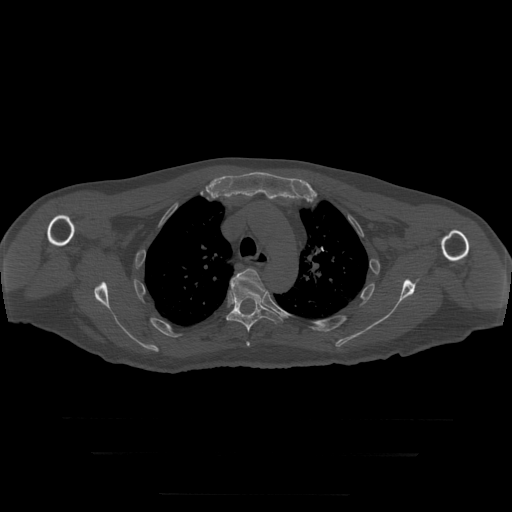
CT including the spine, one axial slice. Slice 229 of 397 in the series (ordered by position). Reconstruction kernel STANDARD. Bone window (W 1800 / L 400 HU). 512 × 512 image matrix, field of view 510 × 510 mm. Patient age 73 years. Case-level facts recorded for this patient, not image findings: primary cancer: prostate.
Structures marked on this image (semi-automatically segmented with operator editing):
- T4 vertebra: bounding box (x1, y1, x2, y2) in pixels: (231, 269, 266, 346)
- T5 vertebra: (227, 282, 284, 333)